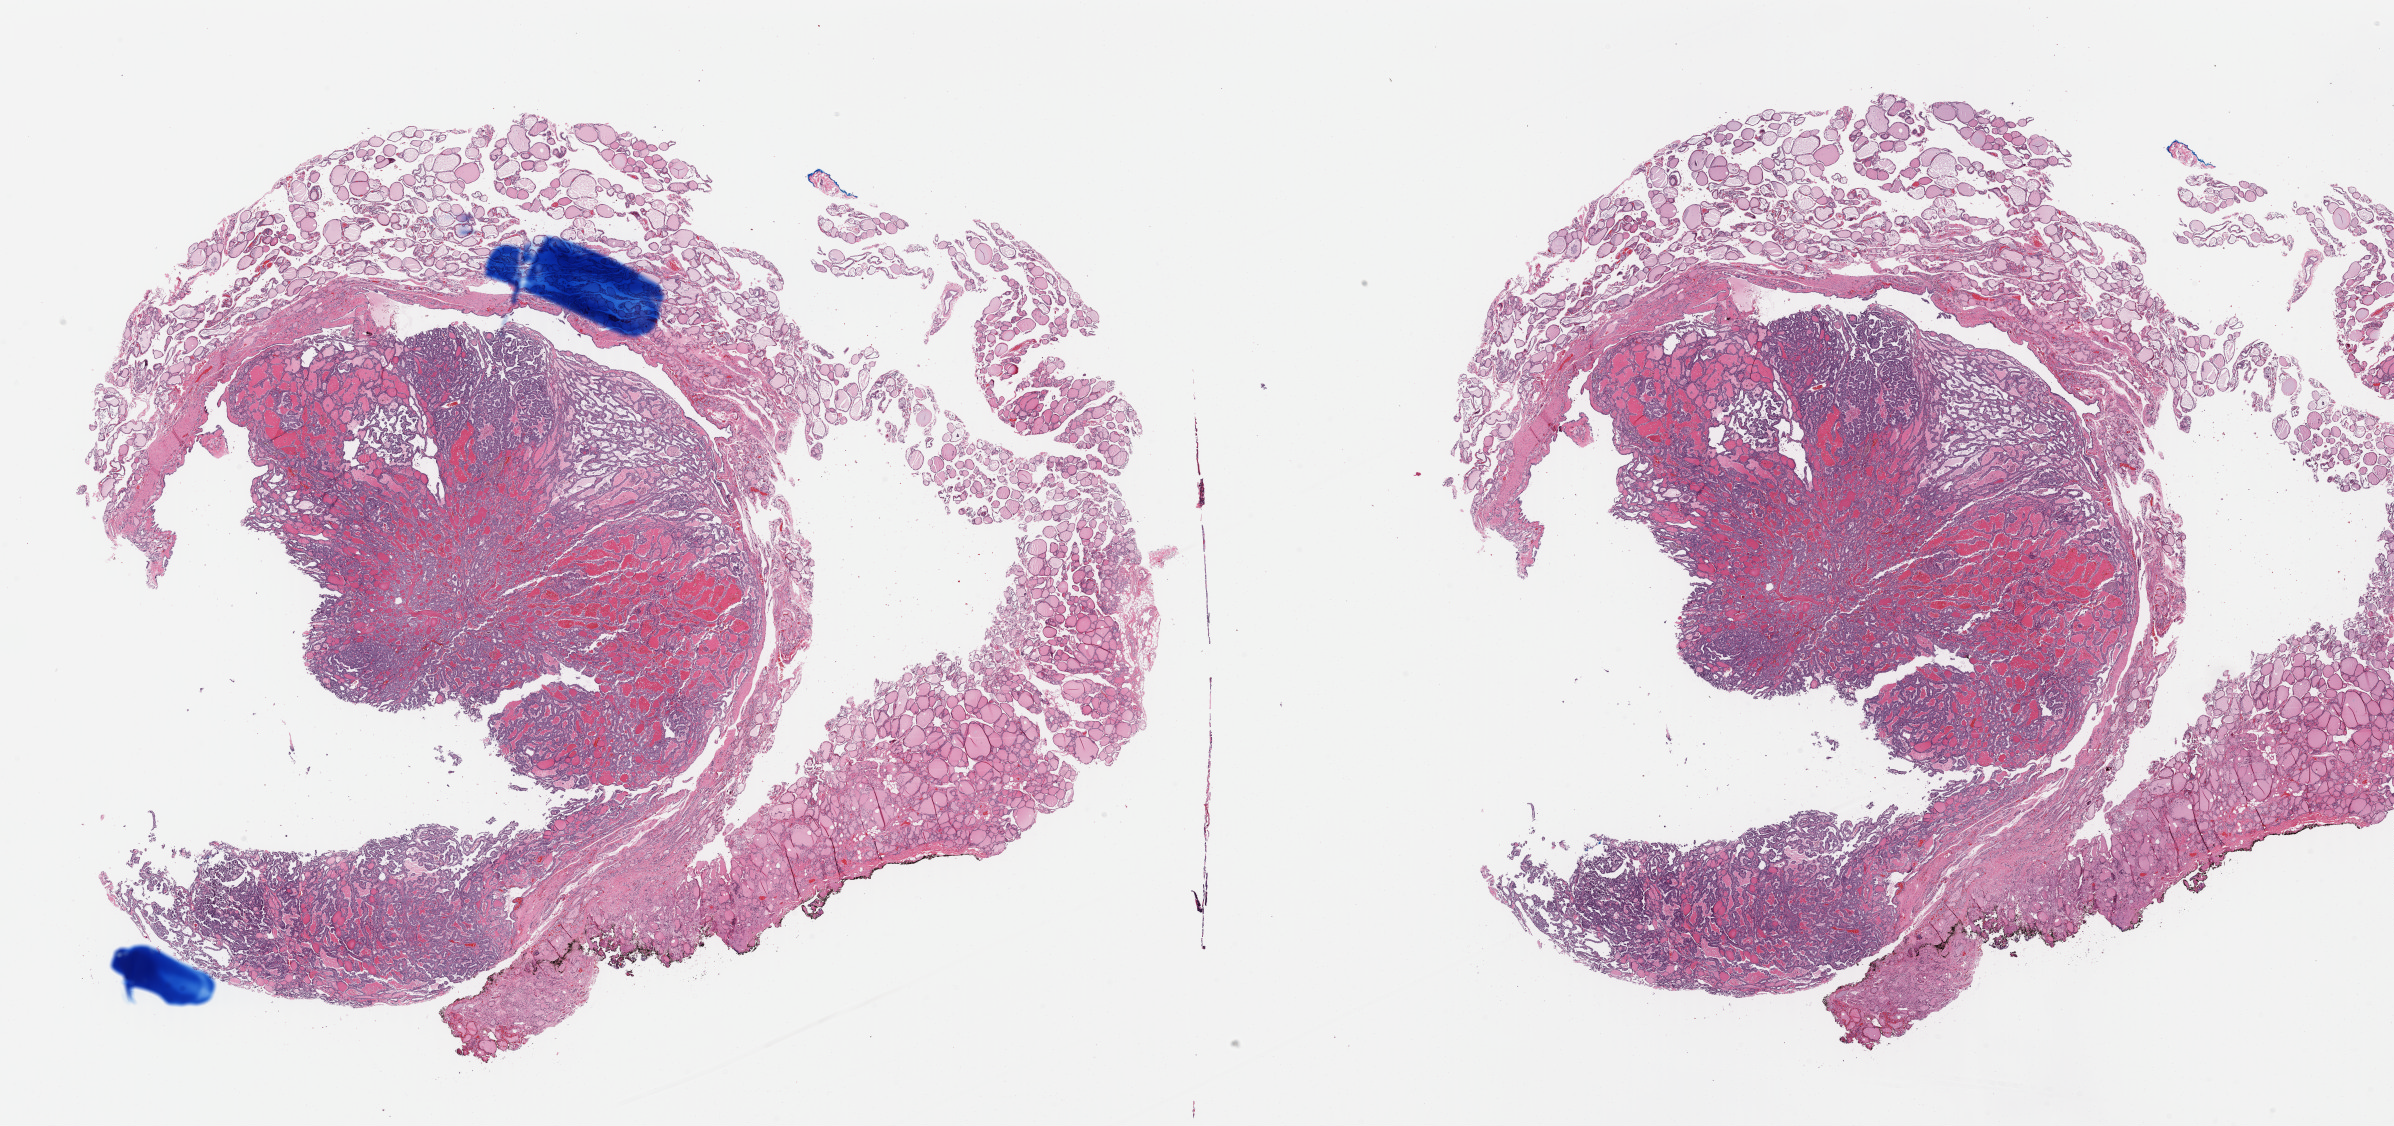
Digitized Hematoxylin and eosin (H&E) stained tissue section (whole slide), low-resolution overview of the scanned area, about 37.8 x 17.8 mm (slide scanned at 40x). Formalin-fixed paraffin-embedded (FFPE) diagnostic section. Primary tumour sample from the thyroid. Female, age 35 years at initial diagnosis.
Pathologic diagnosis: Papillary adenocarcinoma, NOS (thyroid gland).